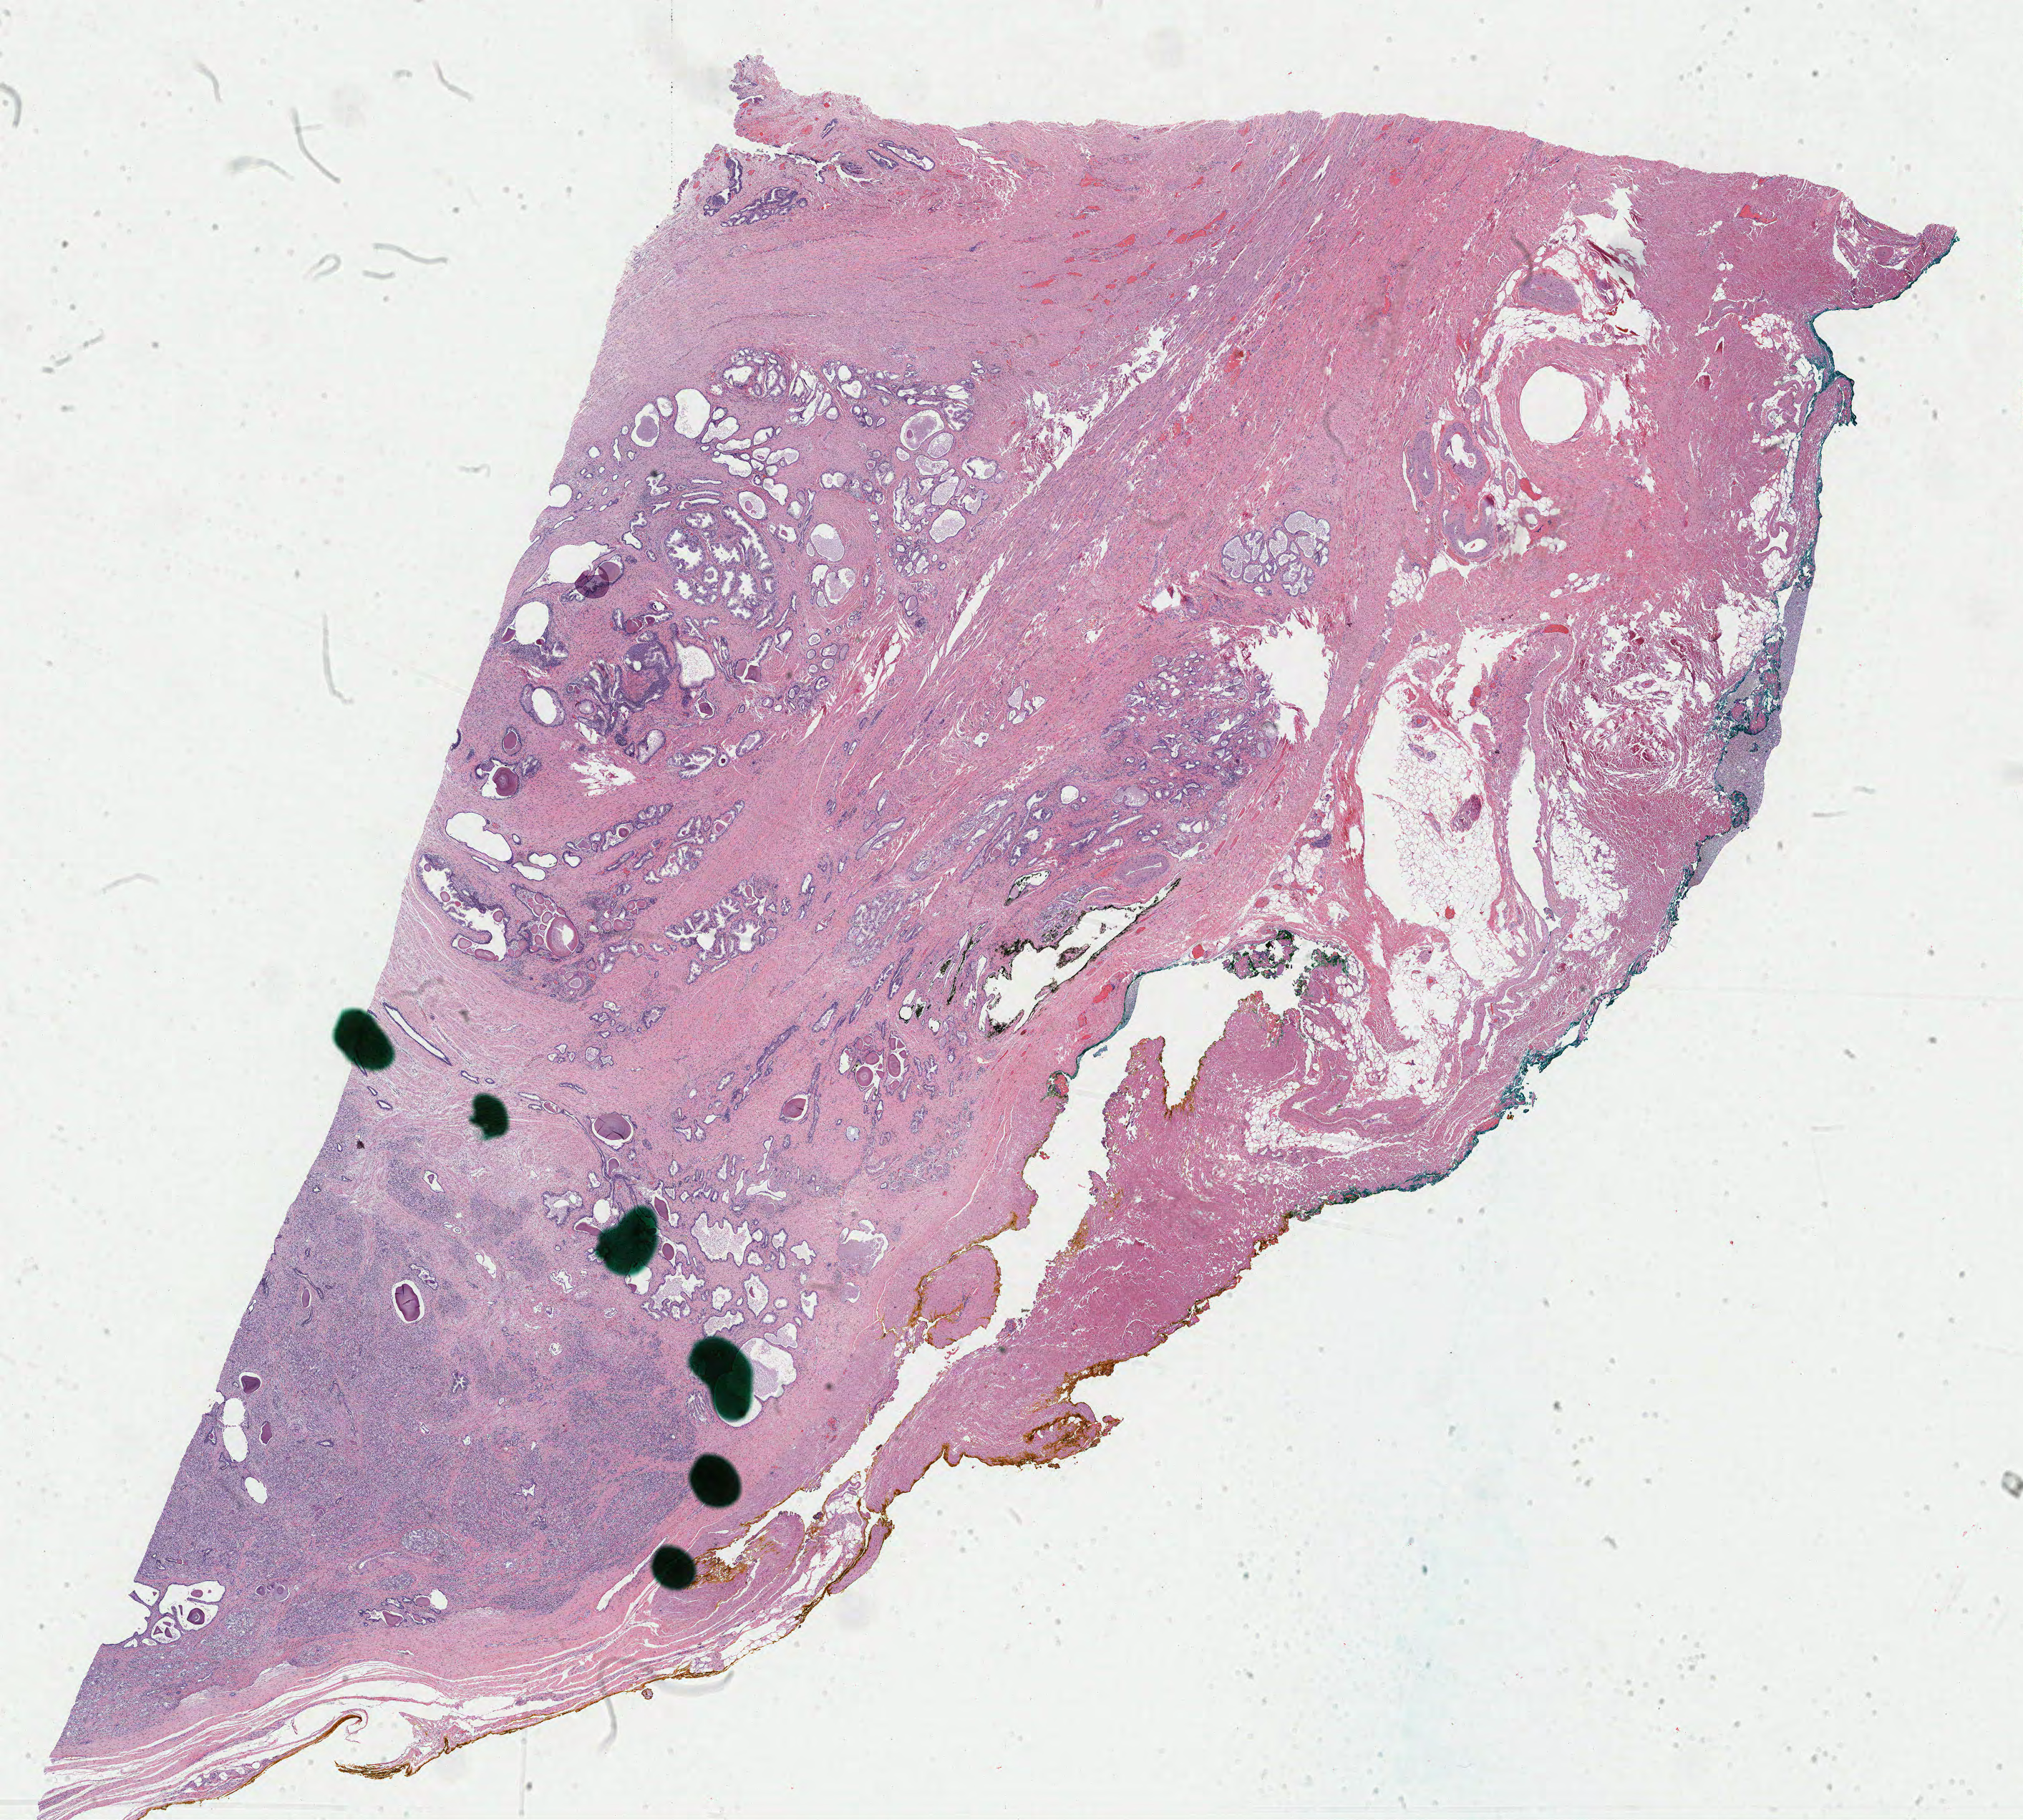
Digitized H&E tissue section (whole slide), shown as a low-resolution overview of the whole scanned area (about 22.4 x 20.2 mm, from a 40x scan), FFPE section, sample: primary tumour, prostate. Patient: male, age at initial diagnosis 61 years. Gleason score: 8 (4+4).
• histologic diagnosis: Adenocarcinoma, NOS (prostate gland)
• laterality: bilateral